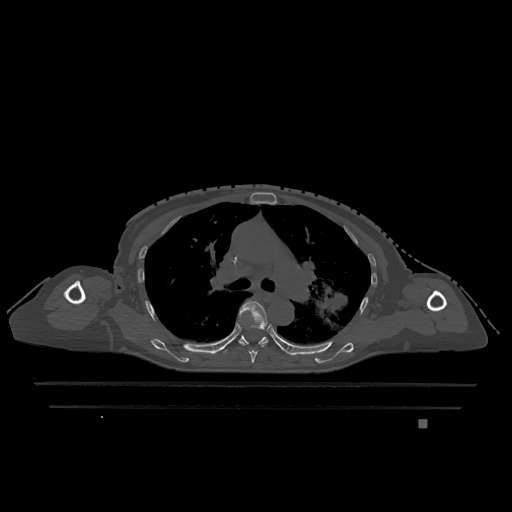
CT including the spine, one axial slice; position 814 of 1317 along the scan axis; bone window (W 1800 / L 400 HU); 0.5 mm slice thickness; 512 × 512 image matrix, field of view 500 × 500 mm. Patient: female, 74 years. Case-level facts recorded for this patient, not image findings: primary cancer: lung; vertebrae with lytic lesions (as recorded): T1, T4, T5, T6, L4, L5.
Outlined on this slice (semi-automatically segmented with operator editing):
- T5 vertebra: bounding box <239,301,268,363> (left, top, right, bottom; pixels)
- T6 vertebra: <224,335,269,352>